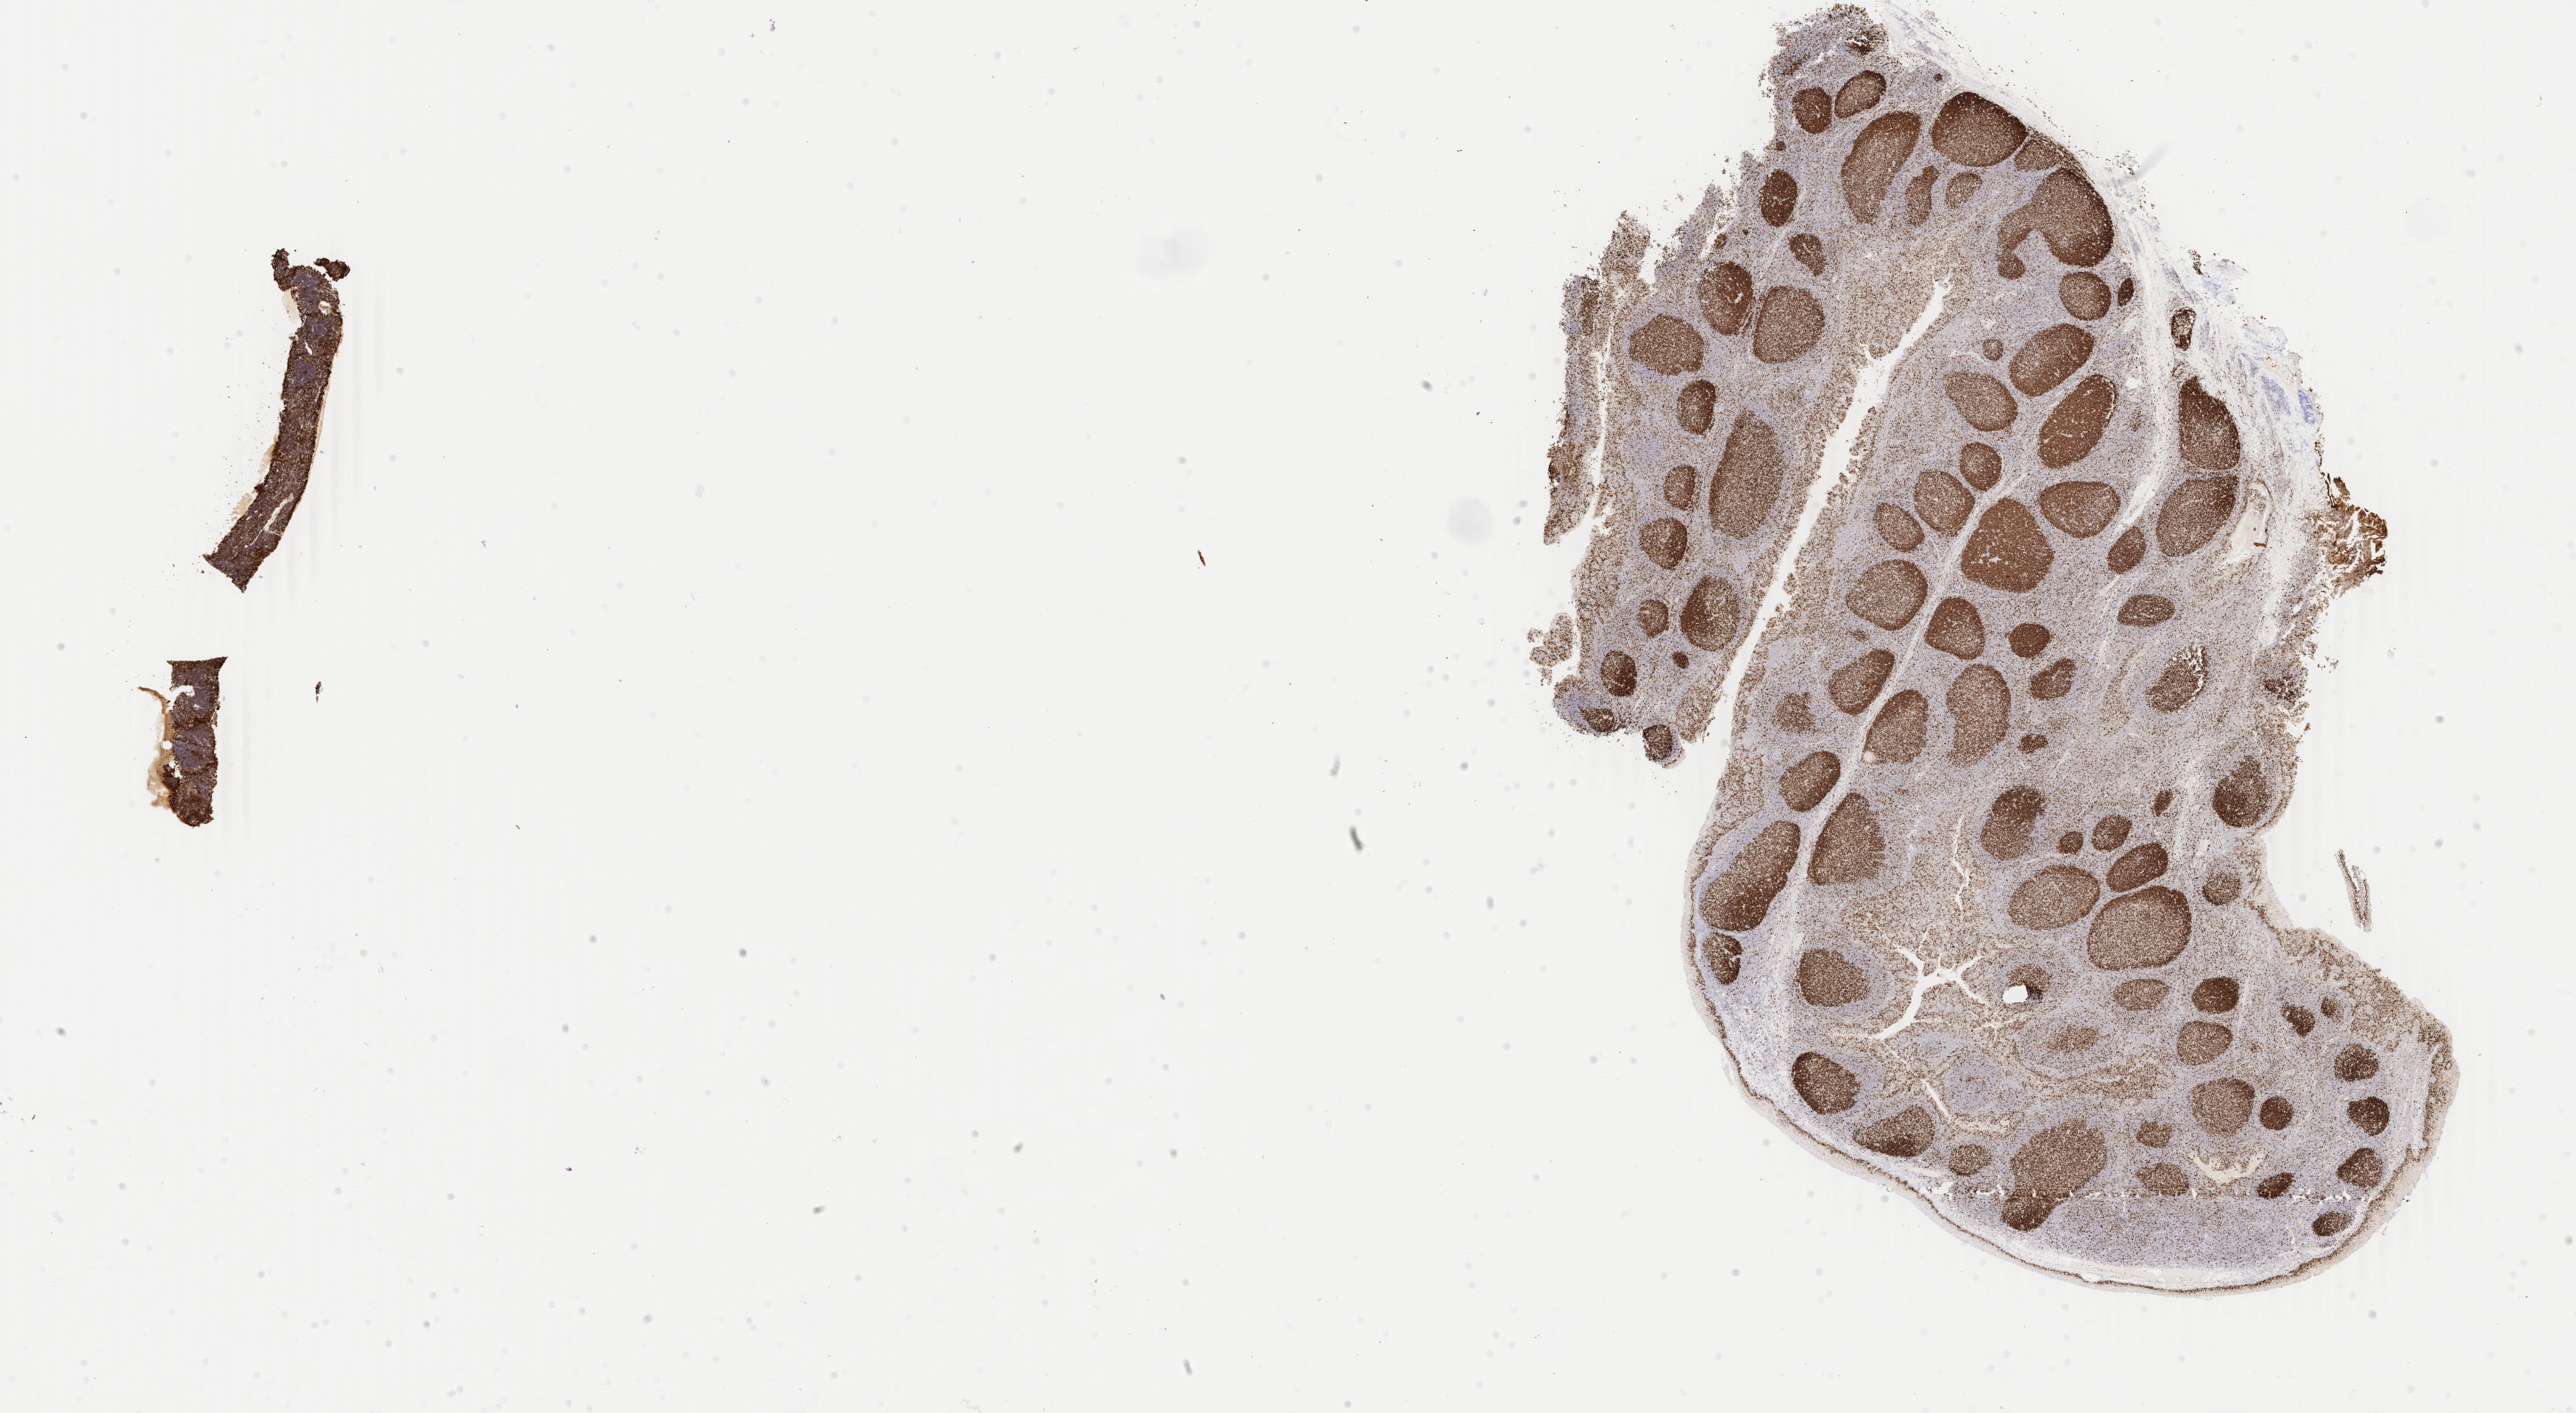
Immunohistochemistry (IHC) whole-slide image stained for Ki-67, a low-resolution overview of the entire scanned area, about 27.8 x 15.3 mm, tumor tissue, anatomic site: abdominal lymph node. Female, age 6 years at initial diagnosis.
Diagnosis: Burkitt lymphoma, NOS.